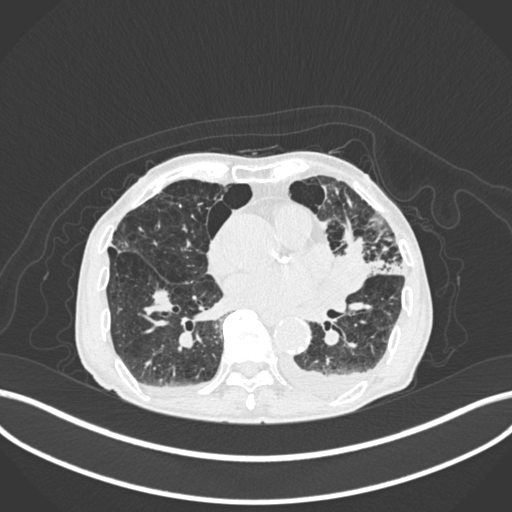
Chest CT, one axial slice; slice 88 of 400 in the series (ordered by position); reconstruction kernel B30f; lung window (W 1500 / L -600 HU); 512 × 512 image matrix, field of view 400 × 400 mm. Patient: male, 90 years or older. Case-level facts recorded for this patient, not image findings: clinical TNM (as recorded): T2b N1 M0.
Structures marked on this image (bounding box drawn by a radiologist):
- lung tumour (recorded histology: squamous cell carcinoma): bounding box <331,240,384,301> (left, top, right, bottom; pixels)